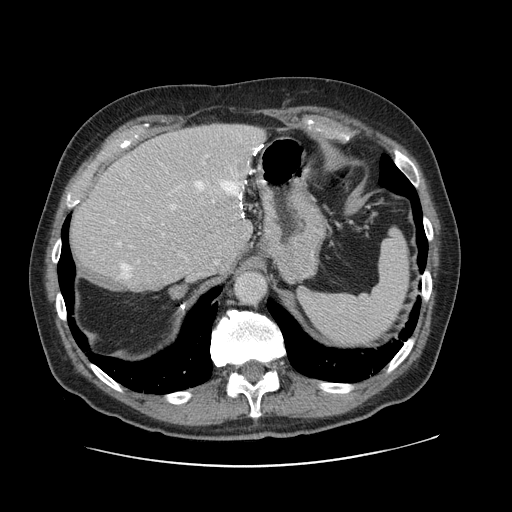
Contrast-enhanced abdominal CT, one axial slice; 120 kVp; intravenous contrast given; soft-tissue window (W 400 / L 40 HU); 2.5 mm slice thickness; 512 × 512 image matrix. Male patient, age 71 years. Case-level facts recorded for this patient, not image findings: diagnosis: colorectal cancer liver metastases, imaged before liver resection; multiple liver metastases: no; largest metastasis: 3.3 cm.
Outlined on this slice (outlined manually by an expert reader):
- hepatic veins: bounding box (x1, y1, x2, y2) in pixels: (121, 145, 262, 278)
- liver: (70, 124, 265, 292)
- planned liver remnant (the part of the liver to remain after resection): (70, 153, 241, 292)
- portal vein (with intrahepatic branches): (117, 204, 176, 246)